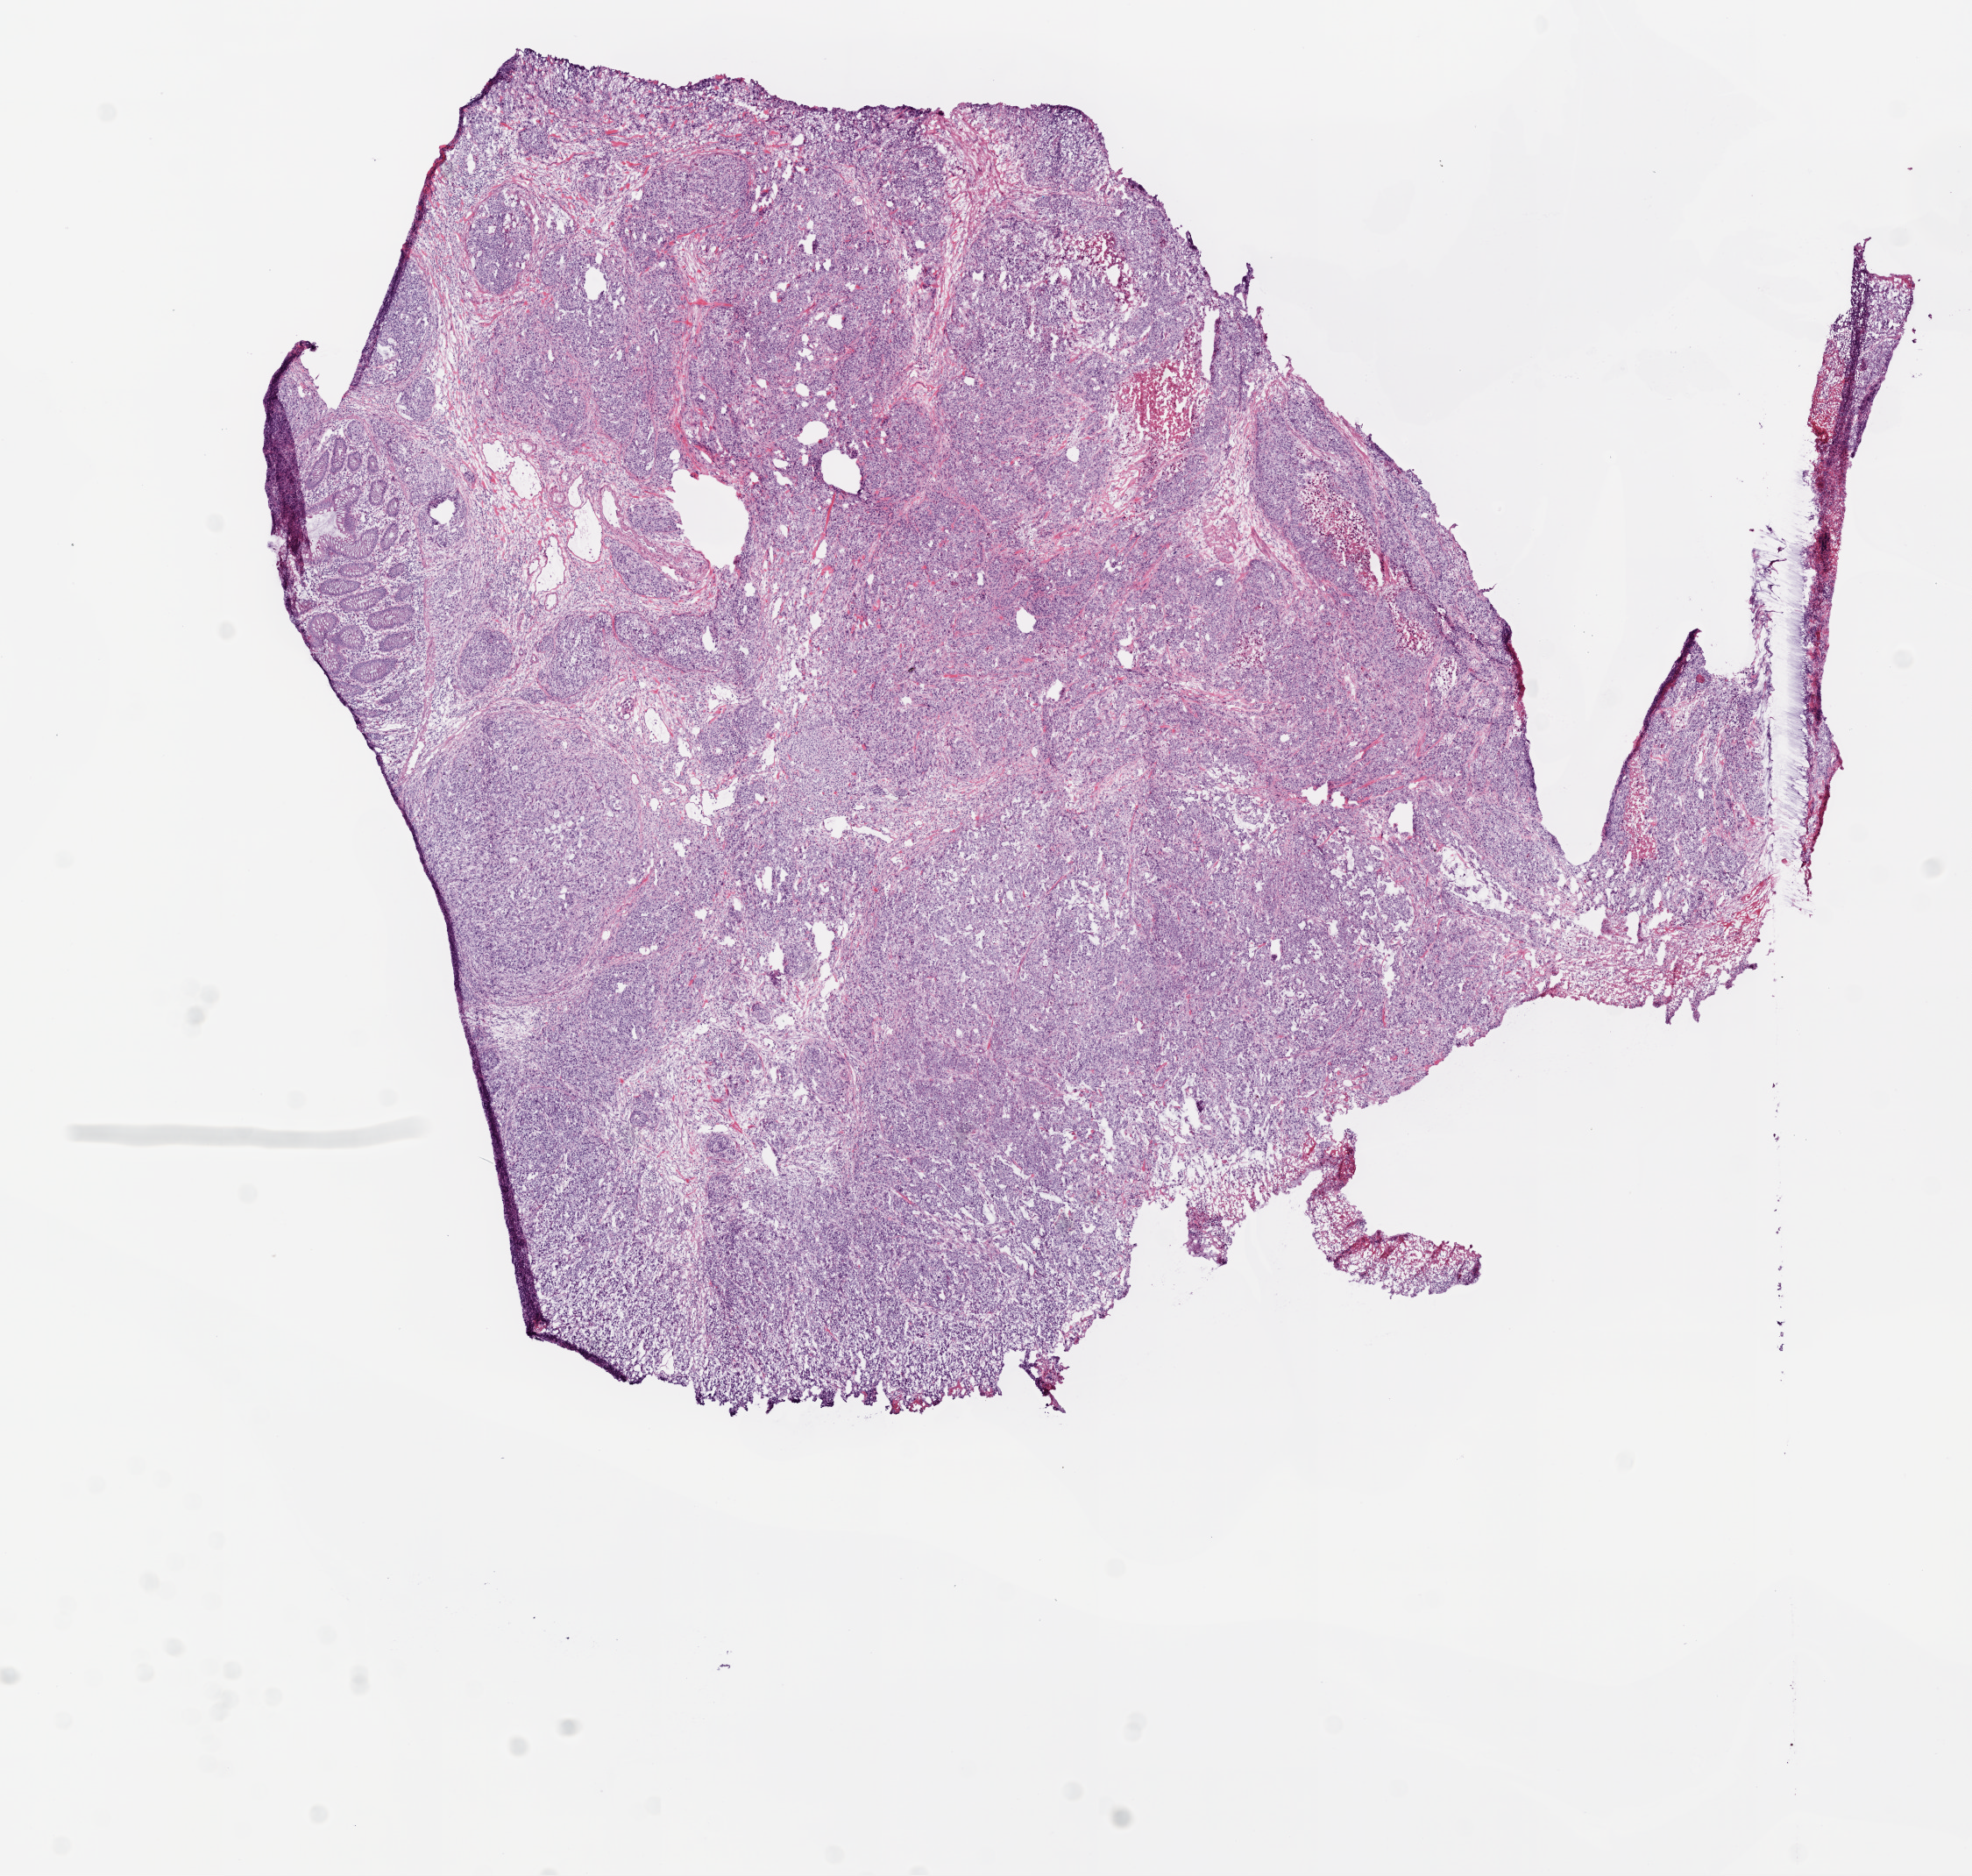
Whole-slide histology image, H&E, shown as a low-resolution overview of the whole scanned area (about 9.0 x 8.6 mm); frozen section from the bottom of the tissue portion; sample: primary tumour, colon. Male, age 66 years at initial diagnosis. Composition of this section per pathologist review: tumour cells 85%, tumour nuclei 85%, normal cells 5%, stromal cells 5%, necrosis 5%.
- histologic diagnosis: Adenocarcinoma, NOS (ascending colon)
- AJCC pathologic stage: IV (6th edition)
- lymph nodes positive (case pathology): 24 of 29 examined